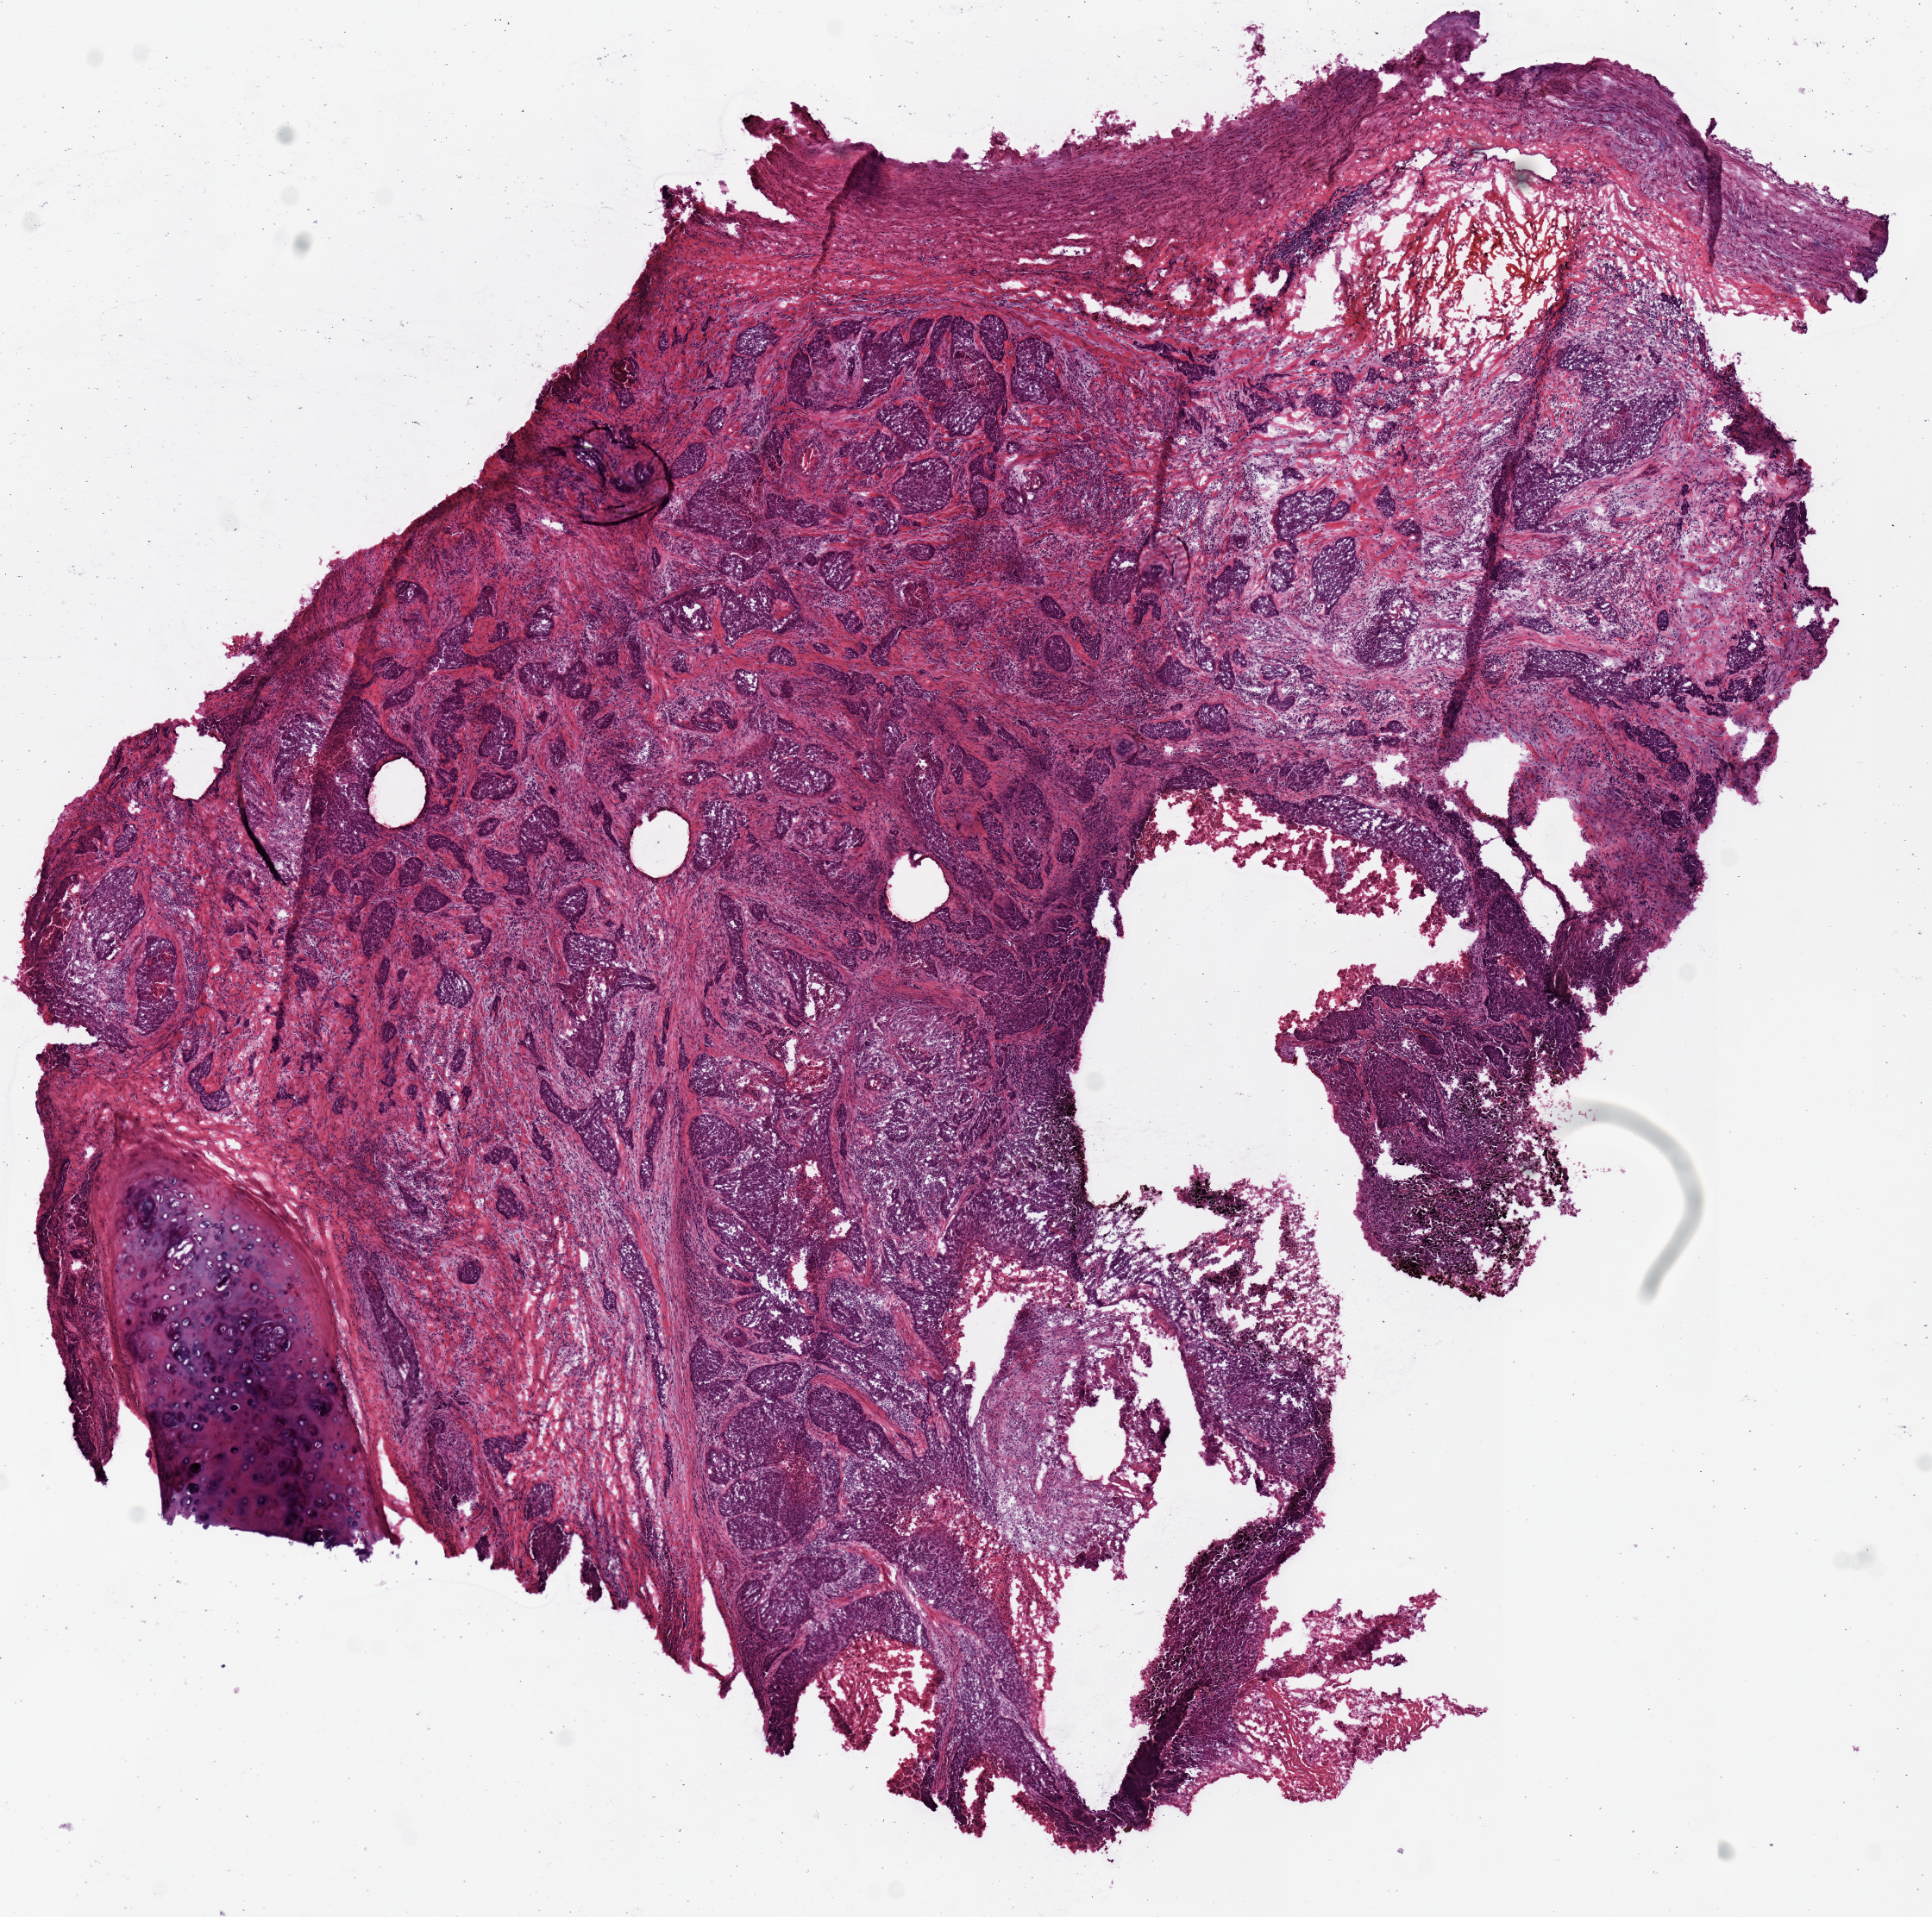
Digitized H&E tissue section (whole slide) — low-resolution overview of the scanned area, about 8.9 x 8.8 mm (from a 20x scan), frozen section, primary tumour sample from the lung. Patient: male, age at initial diagnosis 74 years. Pathologist review of this section (percent, as recorded): tumour nuclei 60%, necrosis 10%.
Diagnosis: Squamous cell carcinoma, NOS.